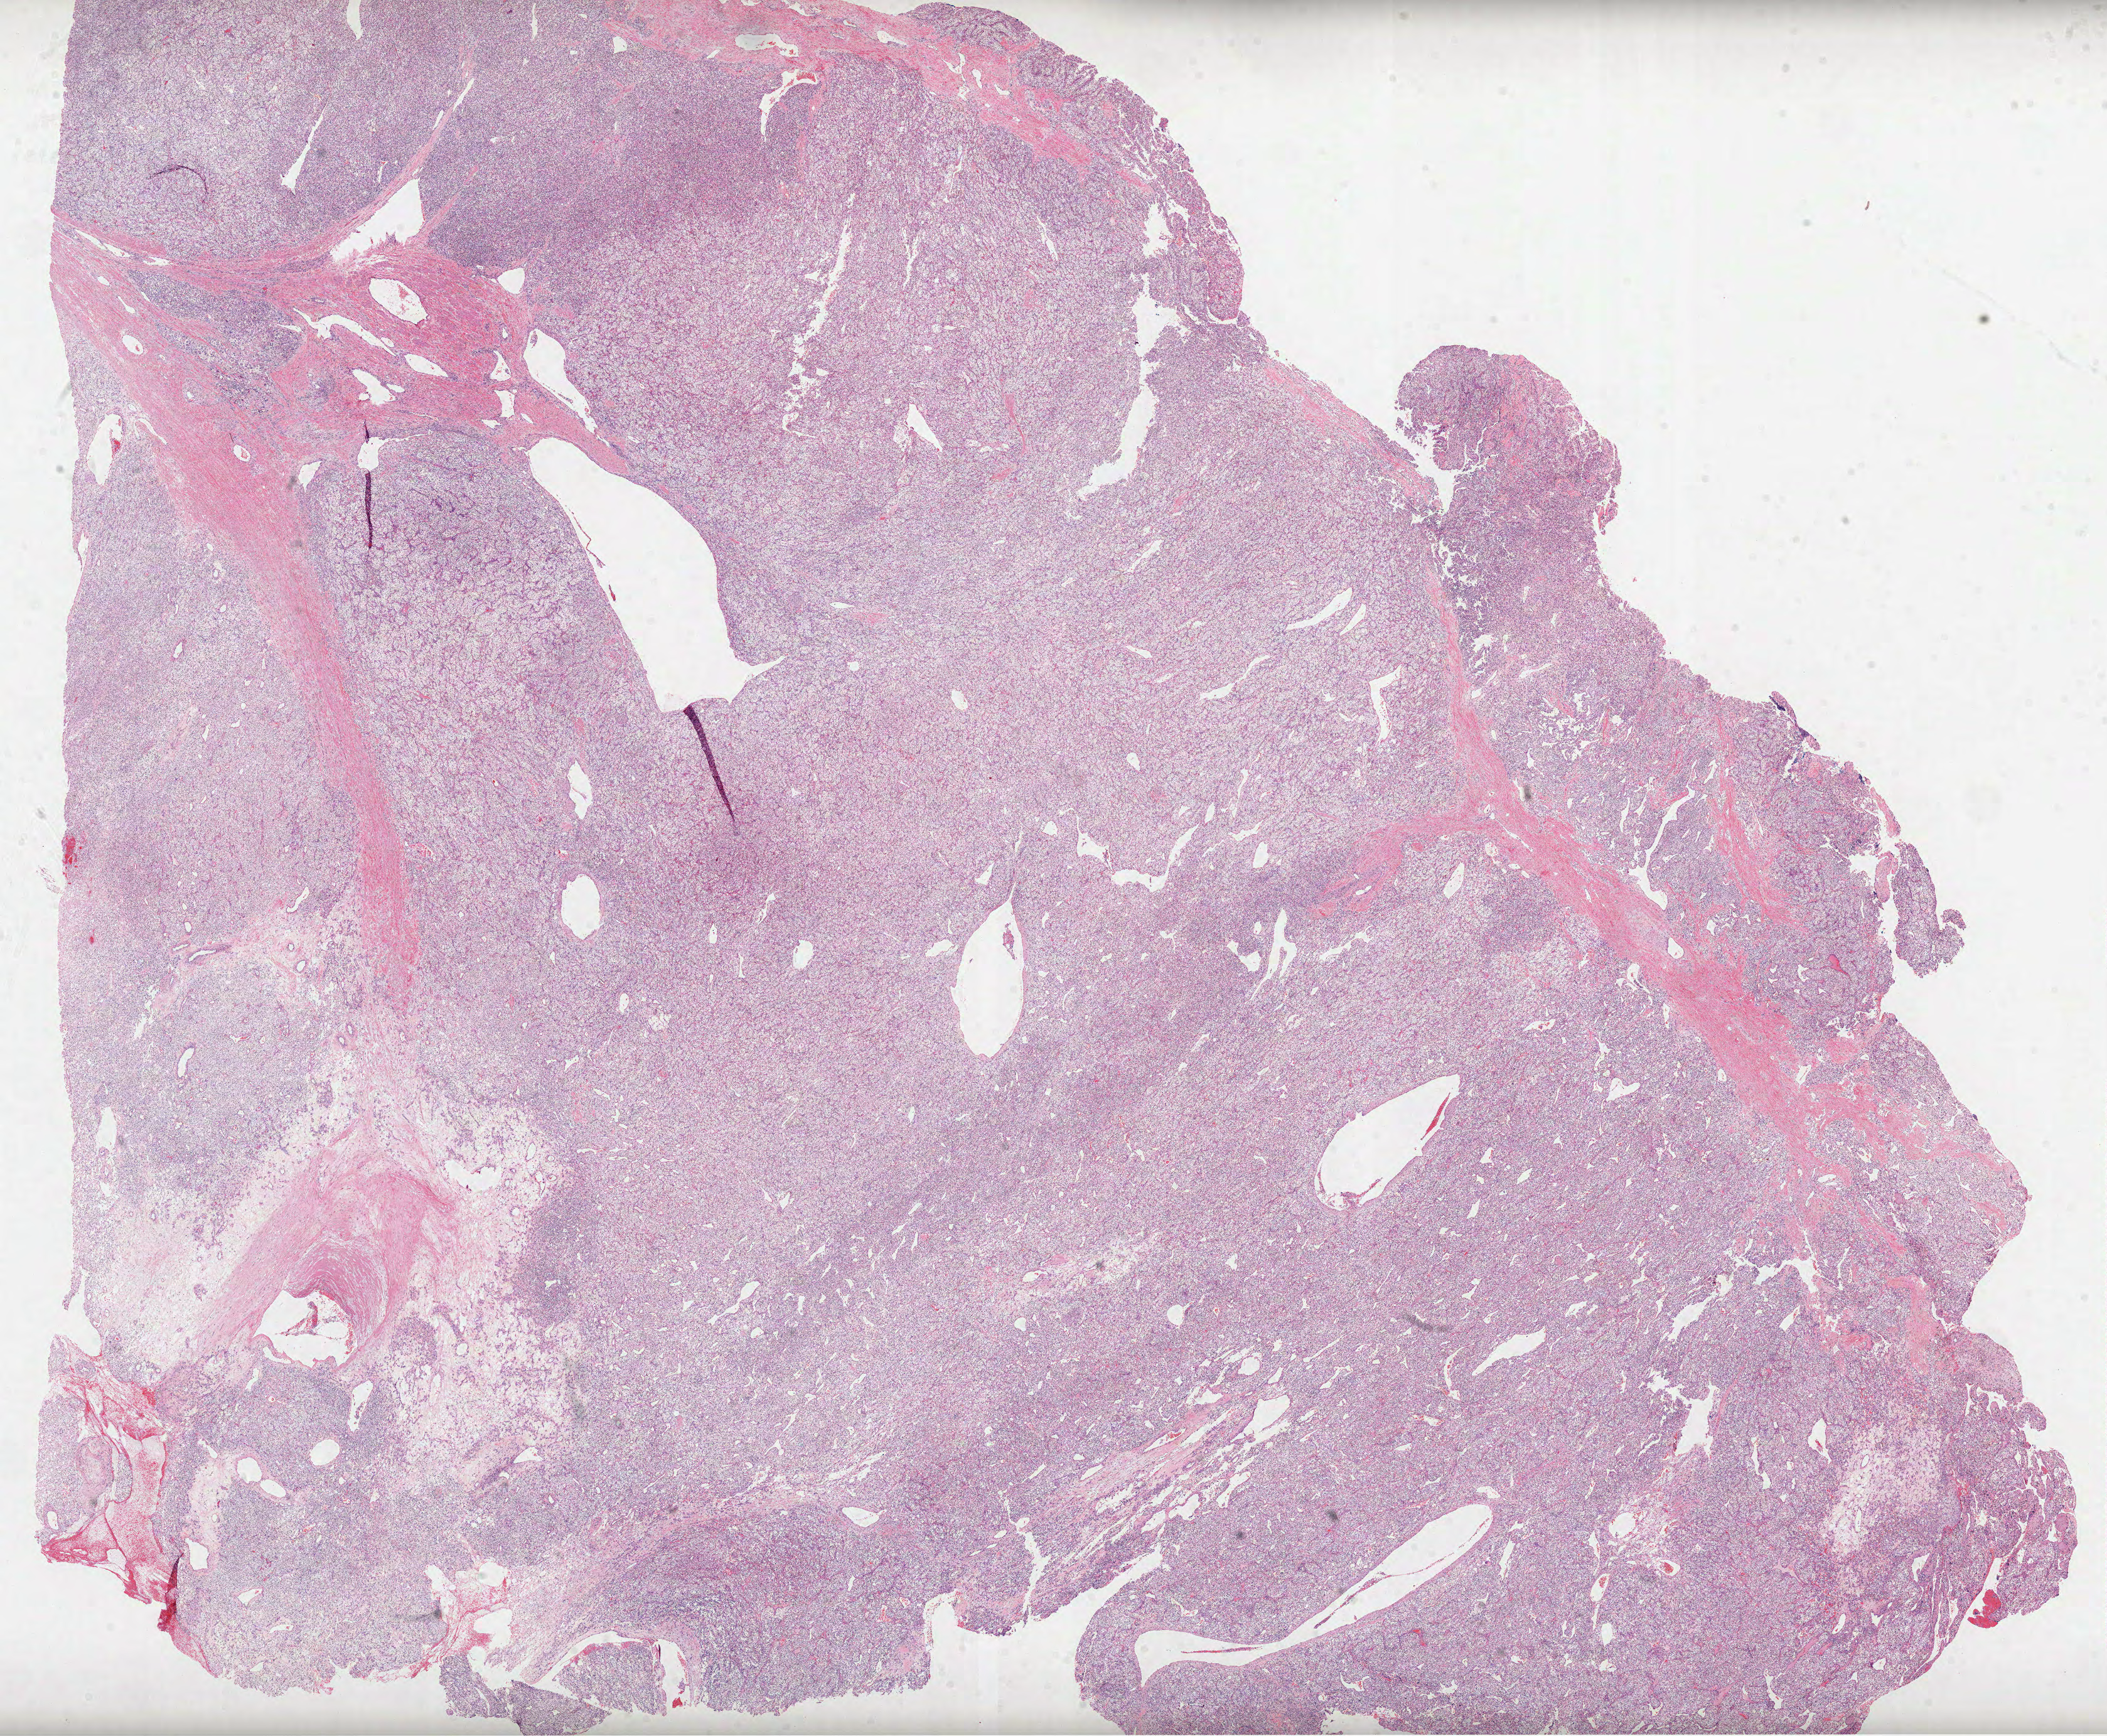
H&E-stained whole-slide image, a low-resolution overview of the entire scanned area, about 27.1 x 22.3 mm (acquisition: 40x scan); formalin-fixed paraffin-embedded (FFPE) diagnostic section; sample: primary tumour, kidney. Male patient; age at initial diagnosis 58 years.
Histologic diagnosis: Clear cell adenocarcinoma, NOS.